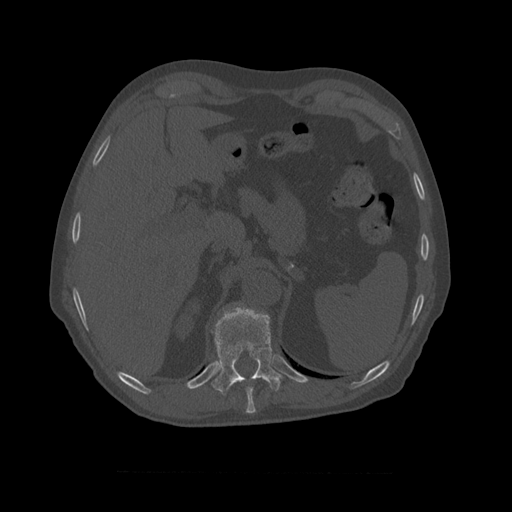
CT including the spine, one axial slice. Slice 405 of 450 in the series (ordered by position). Bone window (W 1800 / L 400 HU). 1.25 mm slice thickness. 512 × 512 image matrix, field of view 405 × 405 mm. Patient age 75 years. From the clinical record (not read from this slice): primary cancer: prostate.
Outlined on this slice (semi-automatic segmentation, software-assisted and operator-edited):
- T10 vertebra: bounding box <211,305,283,396> (left, top, right, bottom; pixels)
- T9 vertebra: <246,387,256,411>